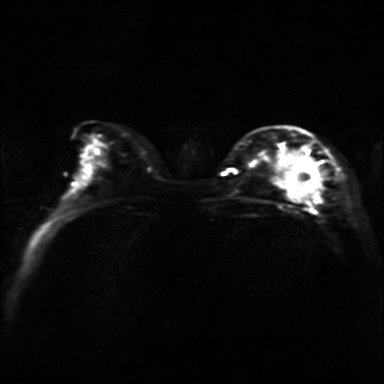
Breast MRI, one axial slice. Slice 14 of 36 in the series (ordered by position). Diffusion-weighted series; image 2 of 4 stored at this slice position (different b-values; order by instance number). 3 T. 384 × 384 image matrix, field of view 320 × 320 mm. Female patient.
Annotated regions visible in this slice (manually delineated by an expert):
- tumour on diffusion-weighted imaging: bounding box [x1, y1, x2, y2] px = [284, 157, 318, 199]